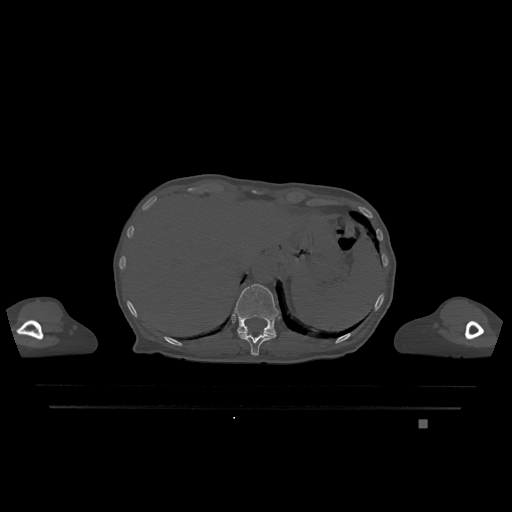
CT including the spine, one axial slice. Position 558 of 1317 along the scan axis. Bone window (W 1800 / L 400 HU). 0.5 mm slice thickness. 512 × 512 image matrix, field of view 500 × 500 mm. Patient: female, 74 years. Case-level facts recorded for this patient, not image findings: primary cancer: lung.
Structures marked on this image (semi-automatic segmentation, software-assisted and operator-edited):
- T11 vertebra: bounding box (x1, y1, x2, y2) in pixels: (238, 333, 276, 356)
- T12 vertebra: (234, 284, 279, 336)